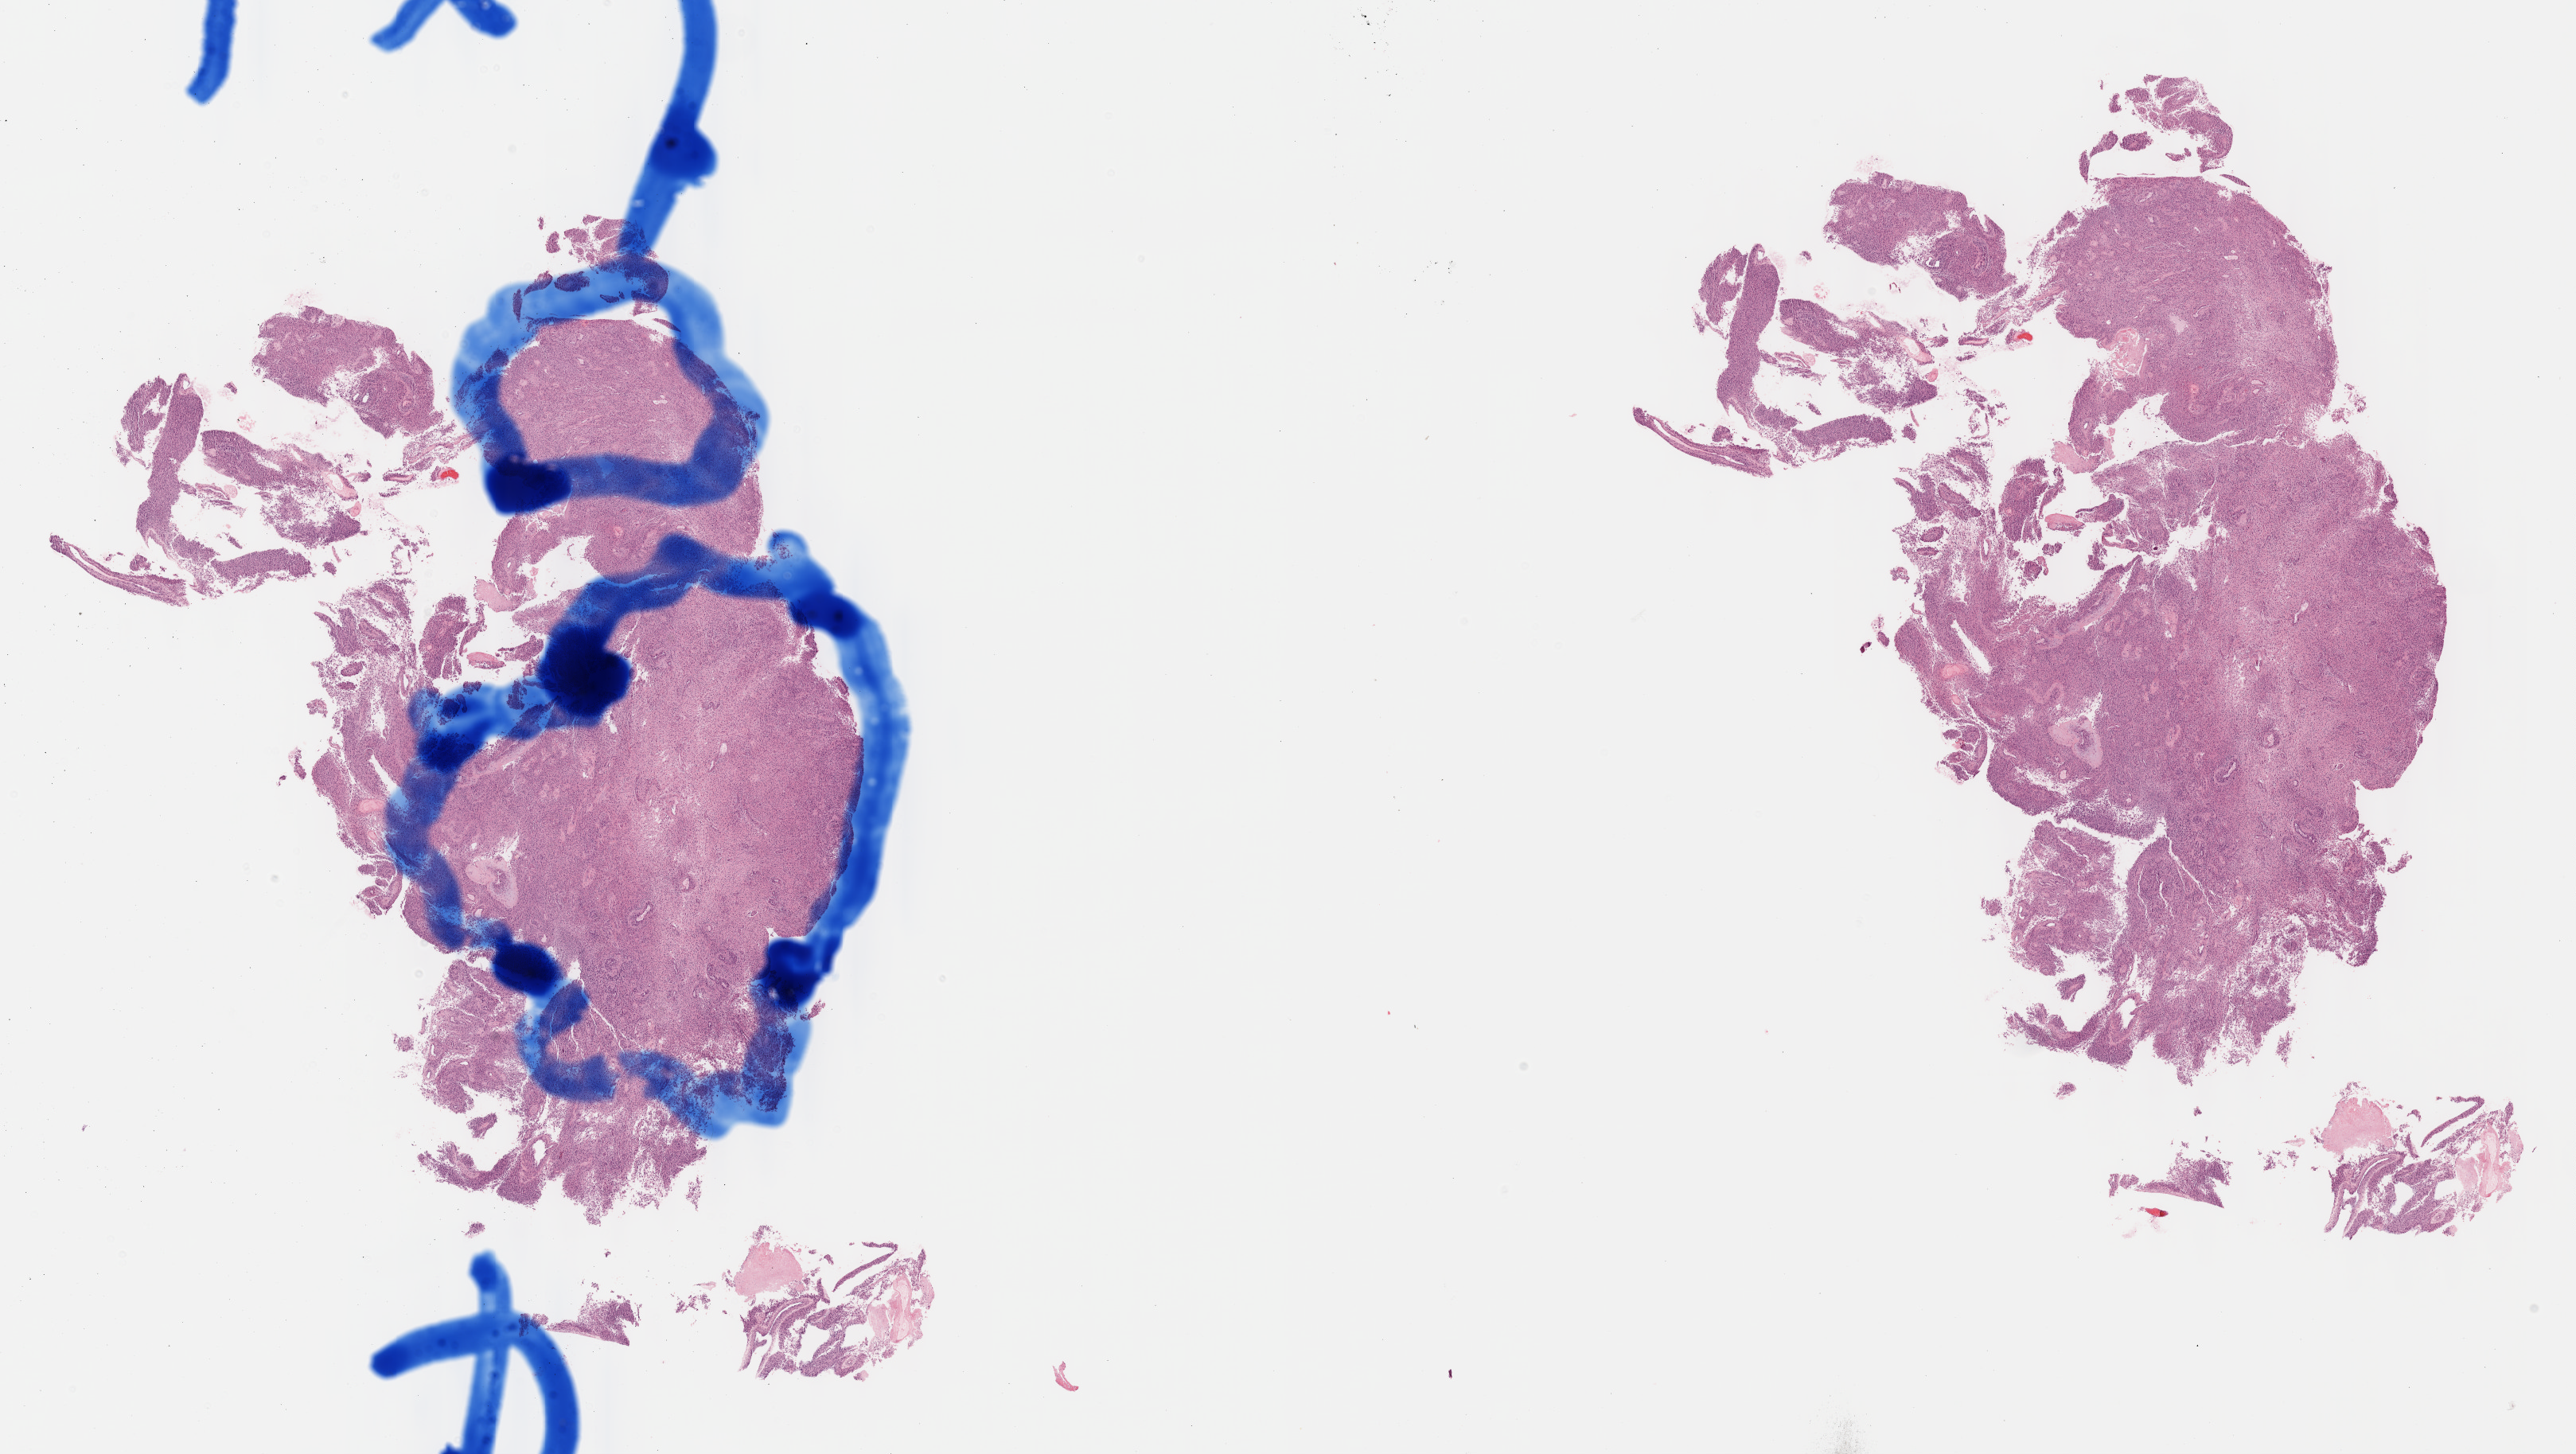
Hematoxylin and eosin (H&E) stained whole-slide image, a low-resolution overview of the entire scanned area, about 26.2 x 14.8 mm; formalin-fixed paraffin-embedded (FFPE) diagnostic section; primary tumour sample from the brain. Male patient; age at initial diagnosis 69 years.
Diagnosis: Glioblastoma.